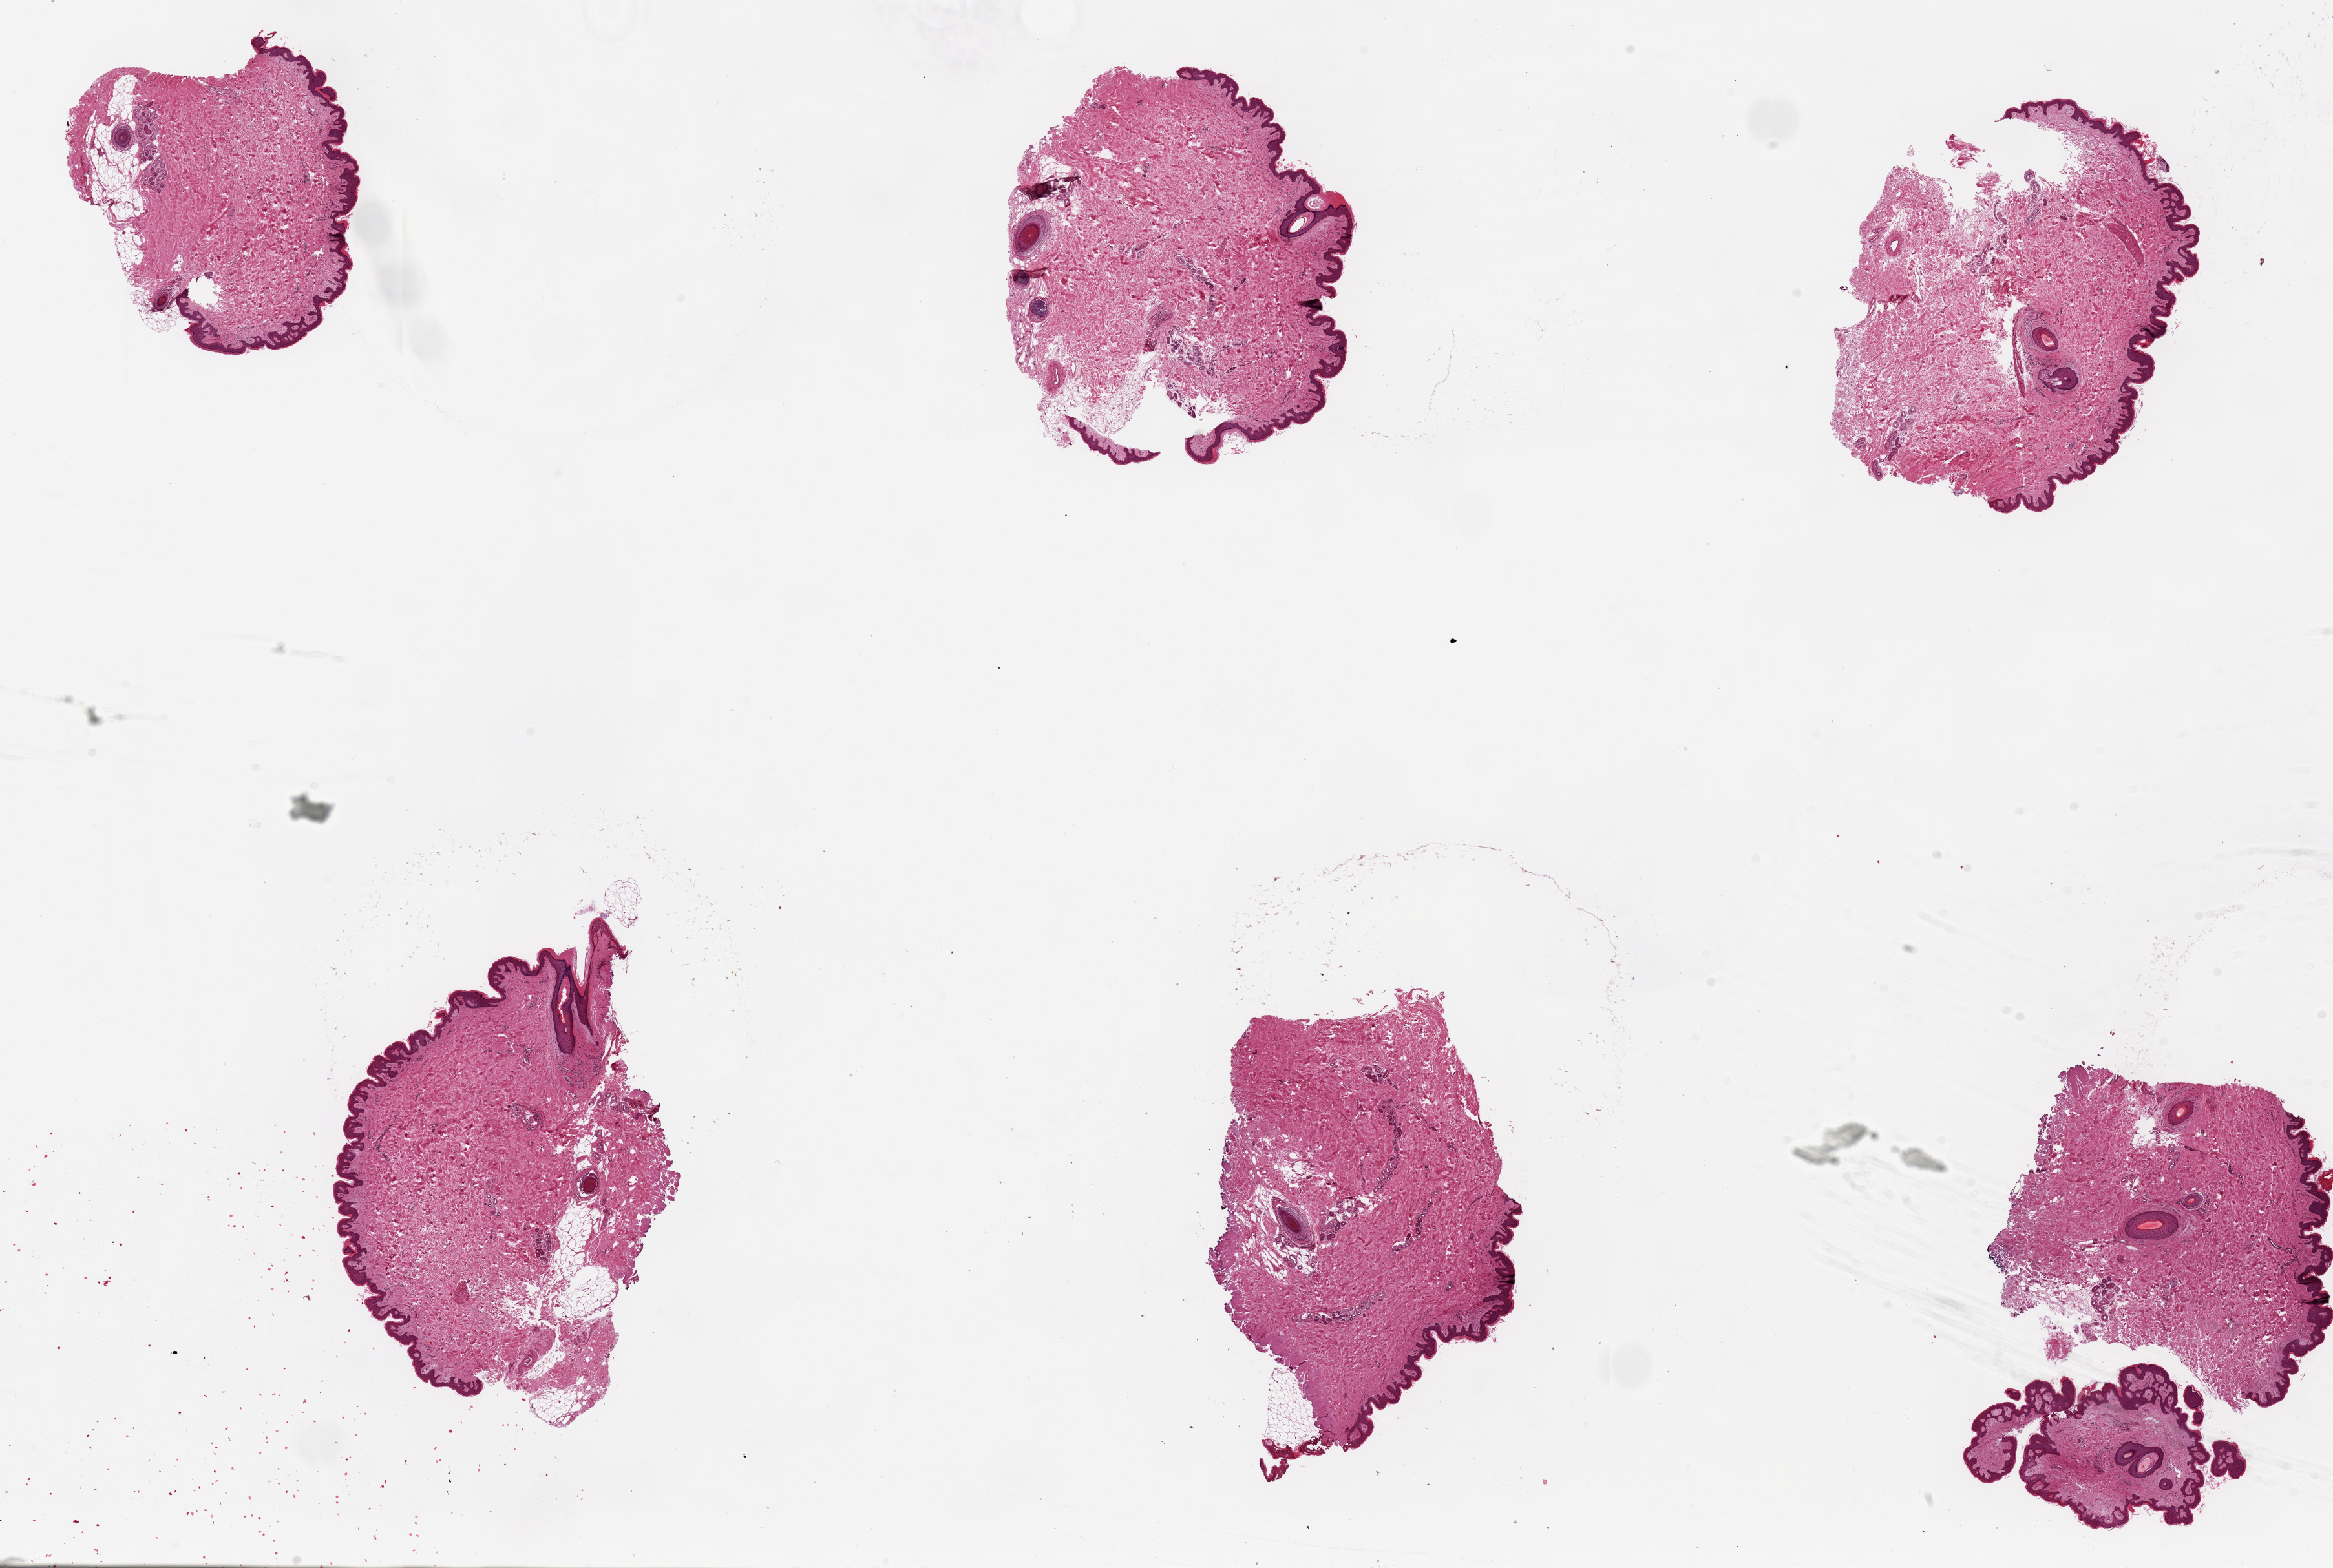
Whole-slide image, hematoxylin and eosin (H&E) stain, low-resolution overview of the scanned area, about 28.5 x 19.2 mm (acquisition: 20x scan); PAXgene-fixed, paraffin-embedded tissue; section of skin of suprapubic region (target tissue); donor tissue sample. Male donor.
Pathologist's review note for this sample: 6 pieces, up to 7x4mm; well trimmed.